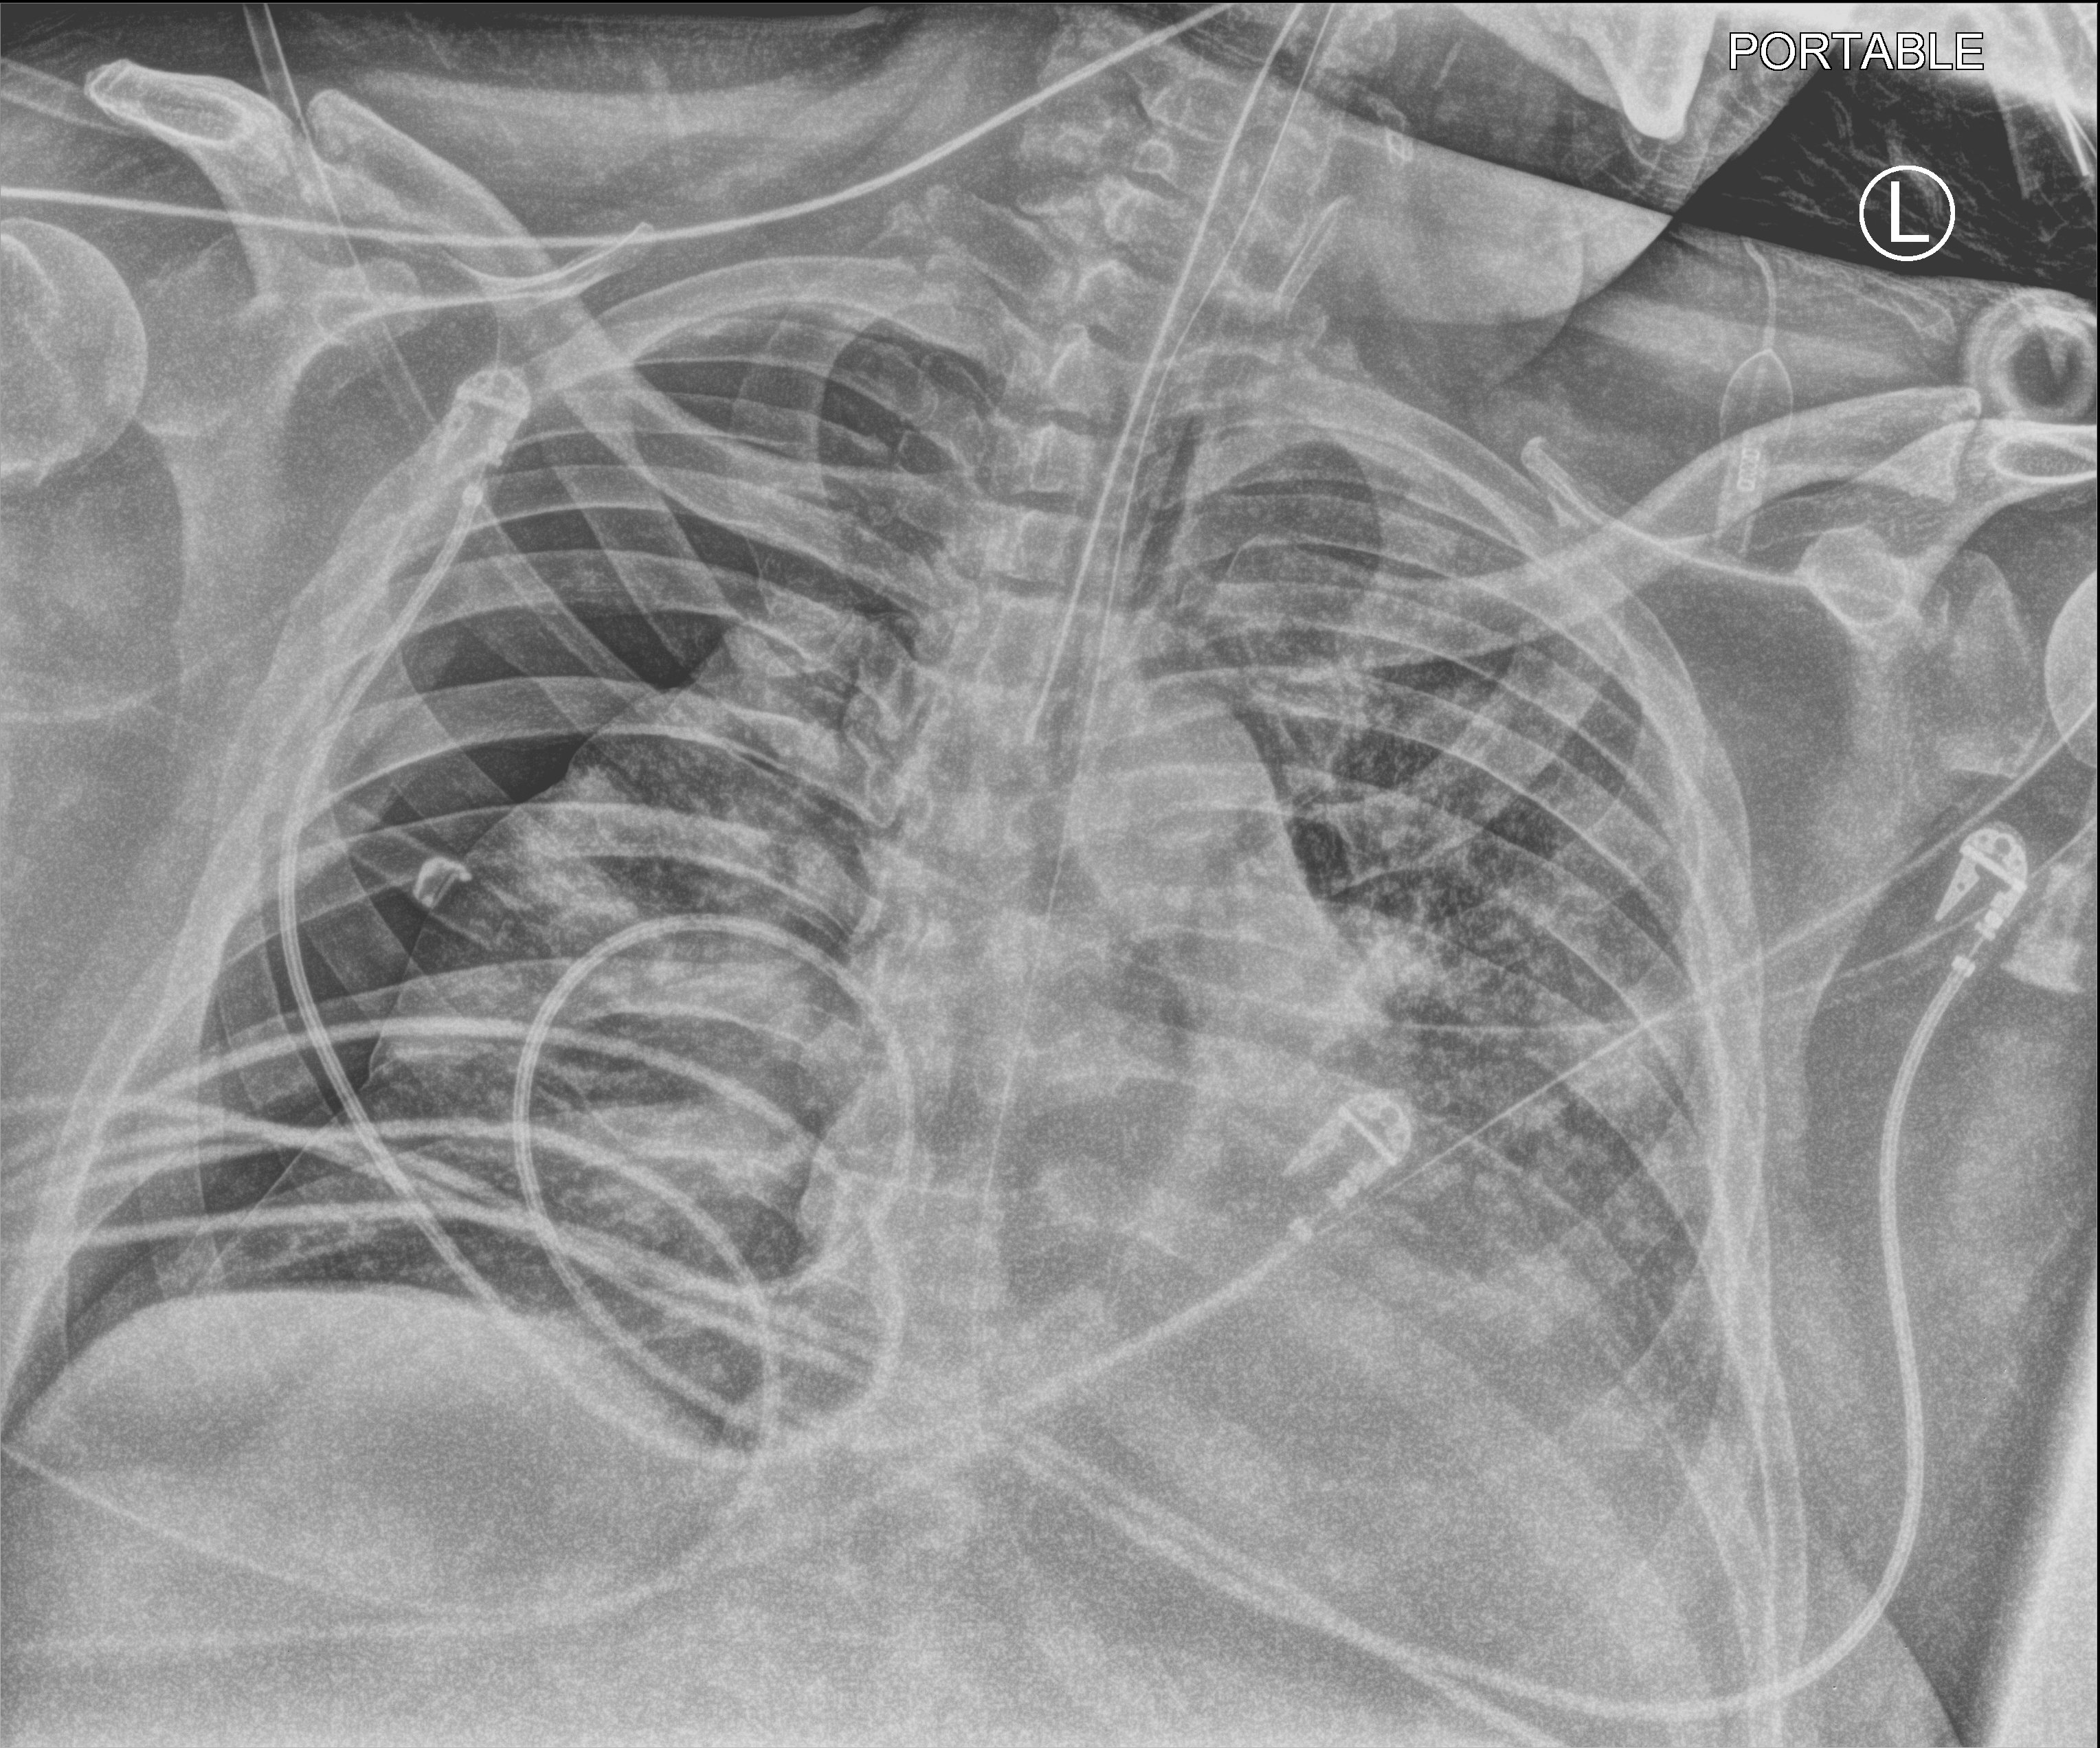
Bedside chest radiograph (computed radiography), anteroposterior (AP) projection. Patient hospitalised with COVID-19; male, aged 60–74 years.
Admission-level facts for this patient (not findings on this image; timing relative to this image not recorded): admitted to intensive care during this hospital stay: yes; hypertension (admission record): yes; COPD (admission record): no.